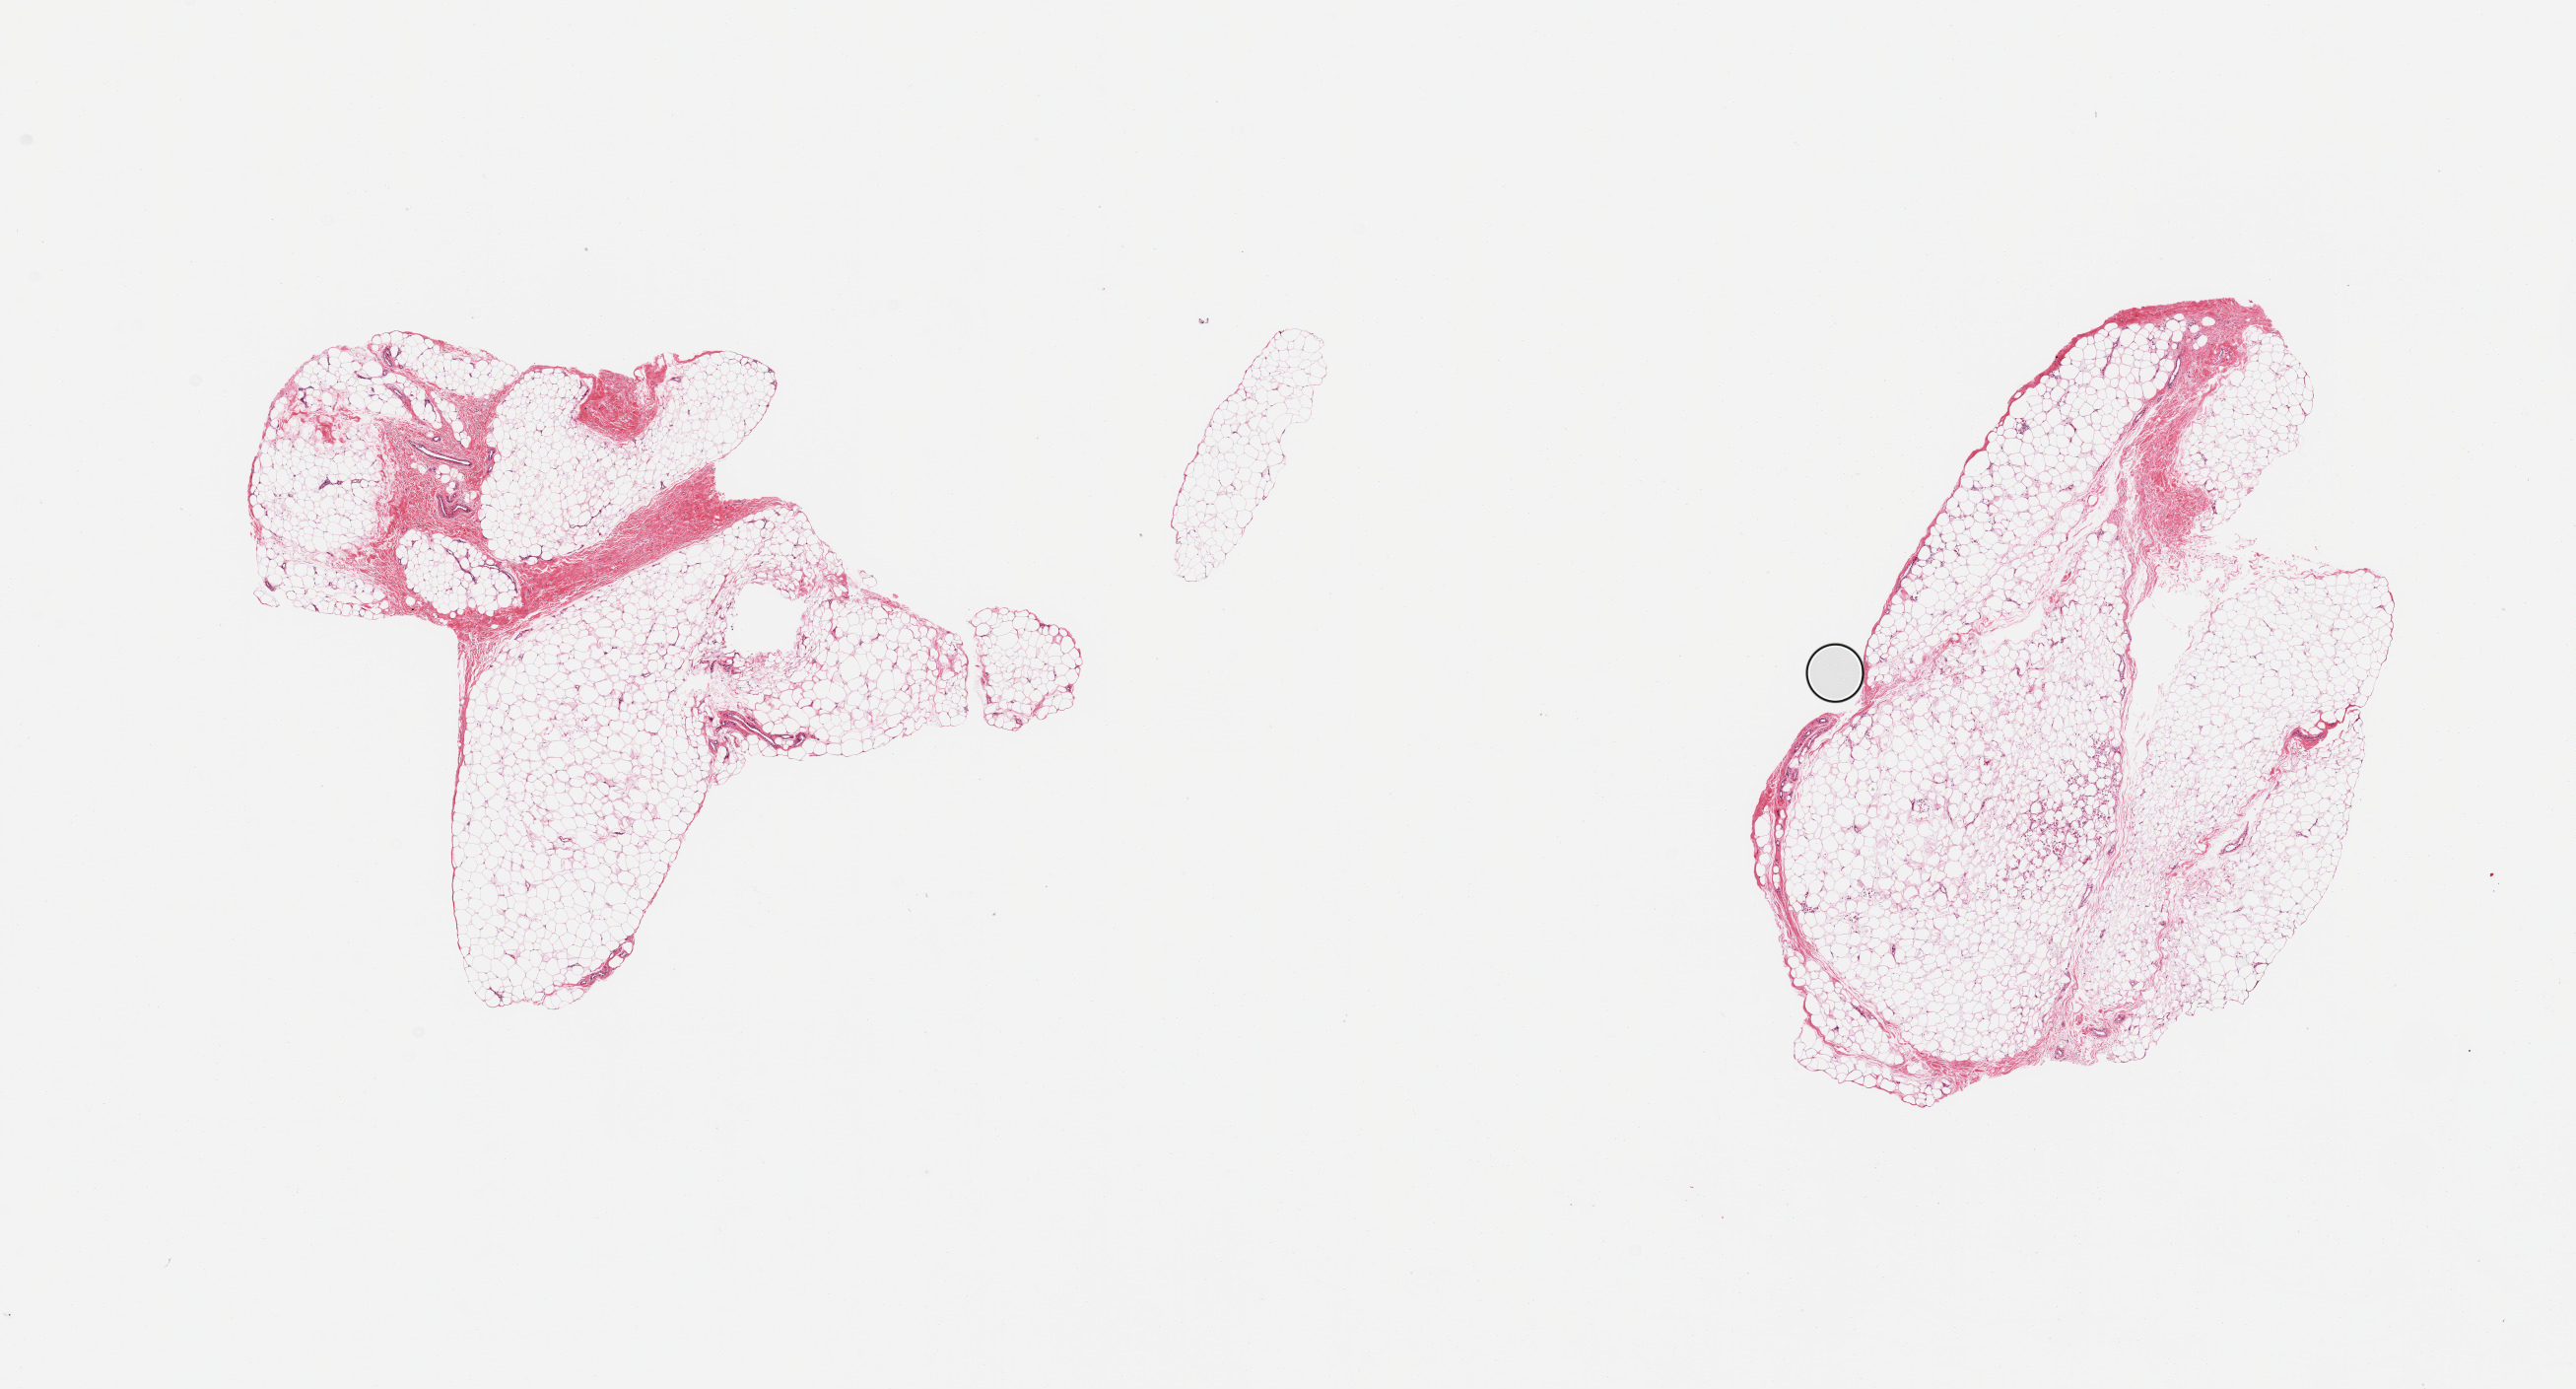
Whole-slide image, haematoxylin and eosin stain, shown as a low-resolution overview of the whole scanned area (about 20.7 x 11.1 mm), PAXgene-fixed, paraffin-embedded tissue, target tissue: adipose tissue, donor tissue sample. Male donor.
Review note (as recorded): 2 pieces; ~10% fibrous component.